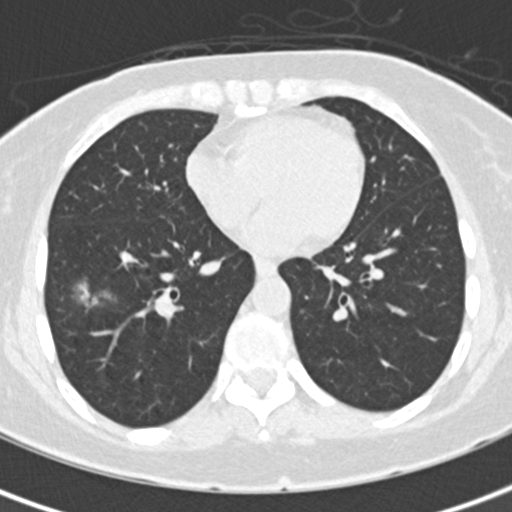
Low-dose screening chest CT, axial slice; first (baseline) screen; lung window (W 1500 / L -600 HU); standard (soft-tissue) reconstruction kernel (B30f). Female, age 56 years at enrolment. Former smoker at enrolment.
• Expert-annotated lung lesion, box from (x=60, y=269) to (x=127, y=326) px.
• The screening reader recorded 5 non-calcified nodules or masses ≥4 mm on this exam (right lower lobe, right upper lobe, left upper lobe, left lower lobe, left lower lobe); which of them this box marks is not recorded.
• Later outcome: lung cancer diagnosed 26 days after this screen — bronchiolo-alveolar carcinoma, mucinous, right lower lobe, well differentiated (G1), stage IA (AJCC 6th edition), 19 mm at pathology.